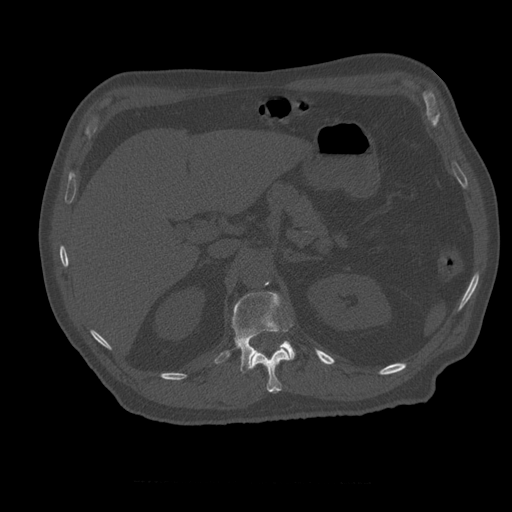
CT including the spine, one axial slice. Bone window (W 1800 / L 400 HU). 1.25 mm slice thickness. 512 × 512 image matrix, field of view 407 × 407 mm. Patient age 73 years. Case-level facts recorded for this patient, not image findings: primary cancer: prostate.
Annotated regions visible in this slice (semi-automatic segmentation, software-assisted and operator-edited):
- L1 vertebra: bounding box <215,292,296,373> (left, top, right, bottom; pixels)
- T12 vertebra: <250,323,293,394>